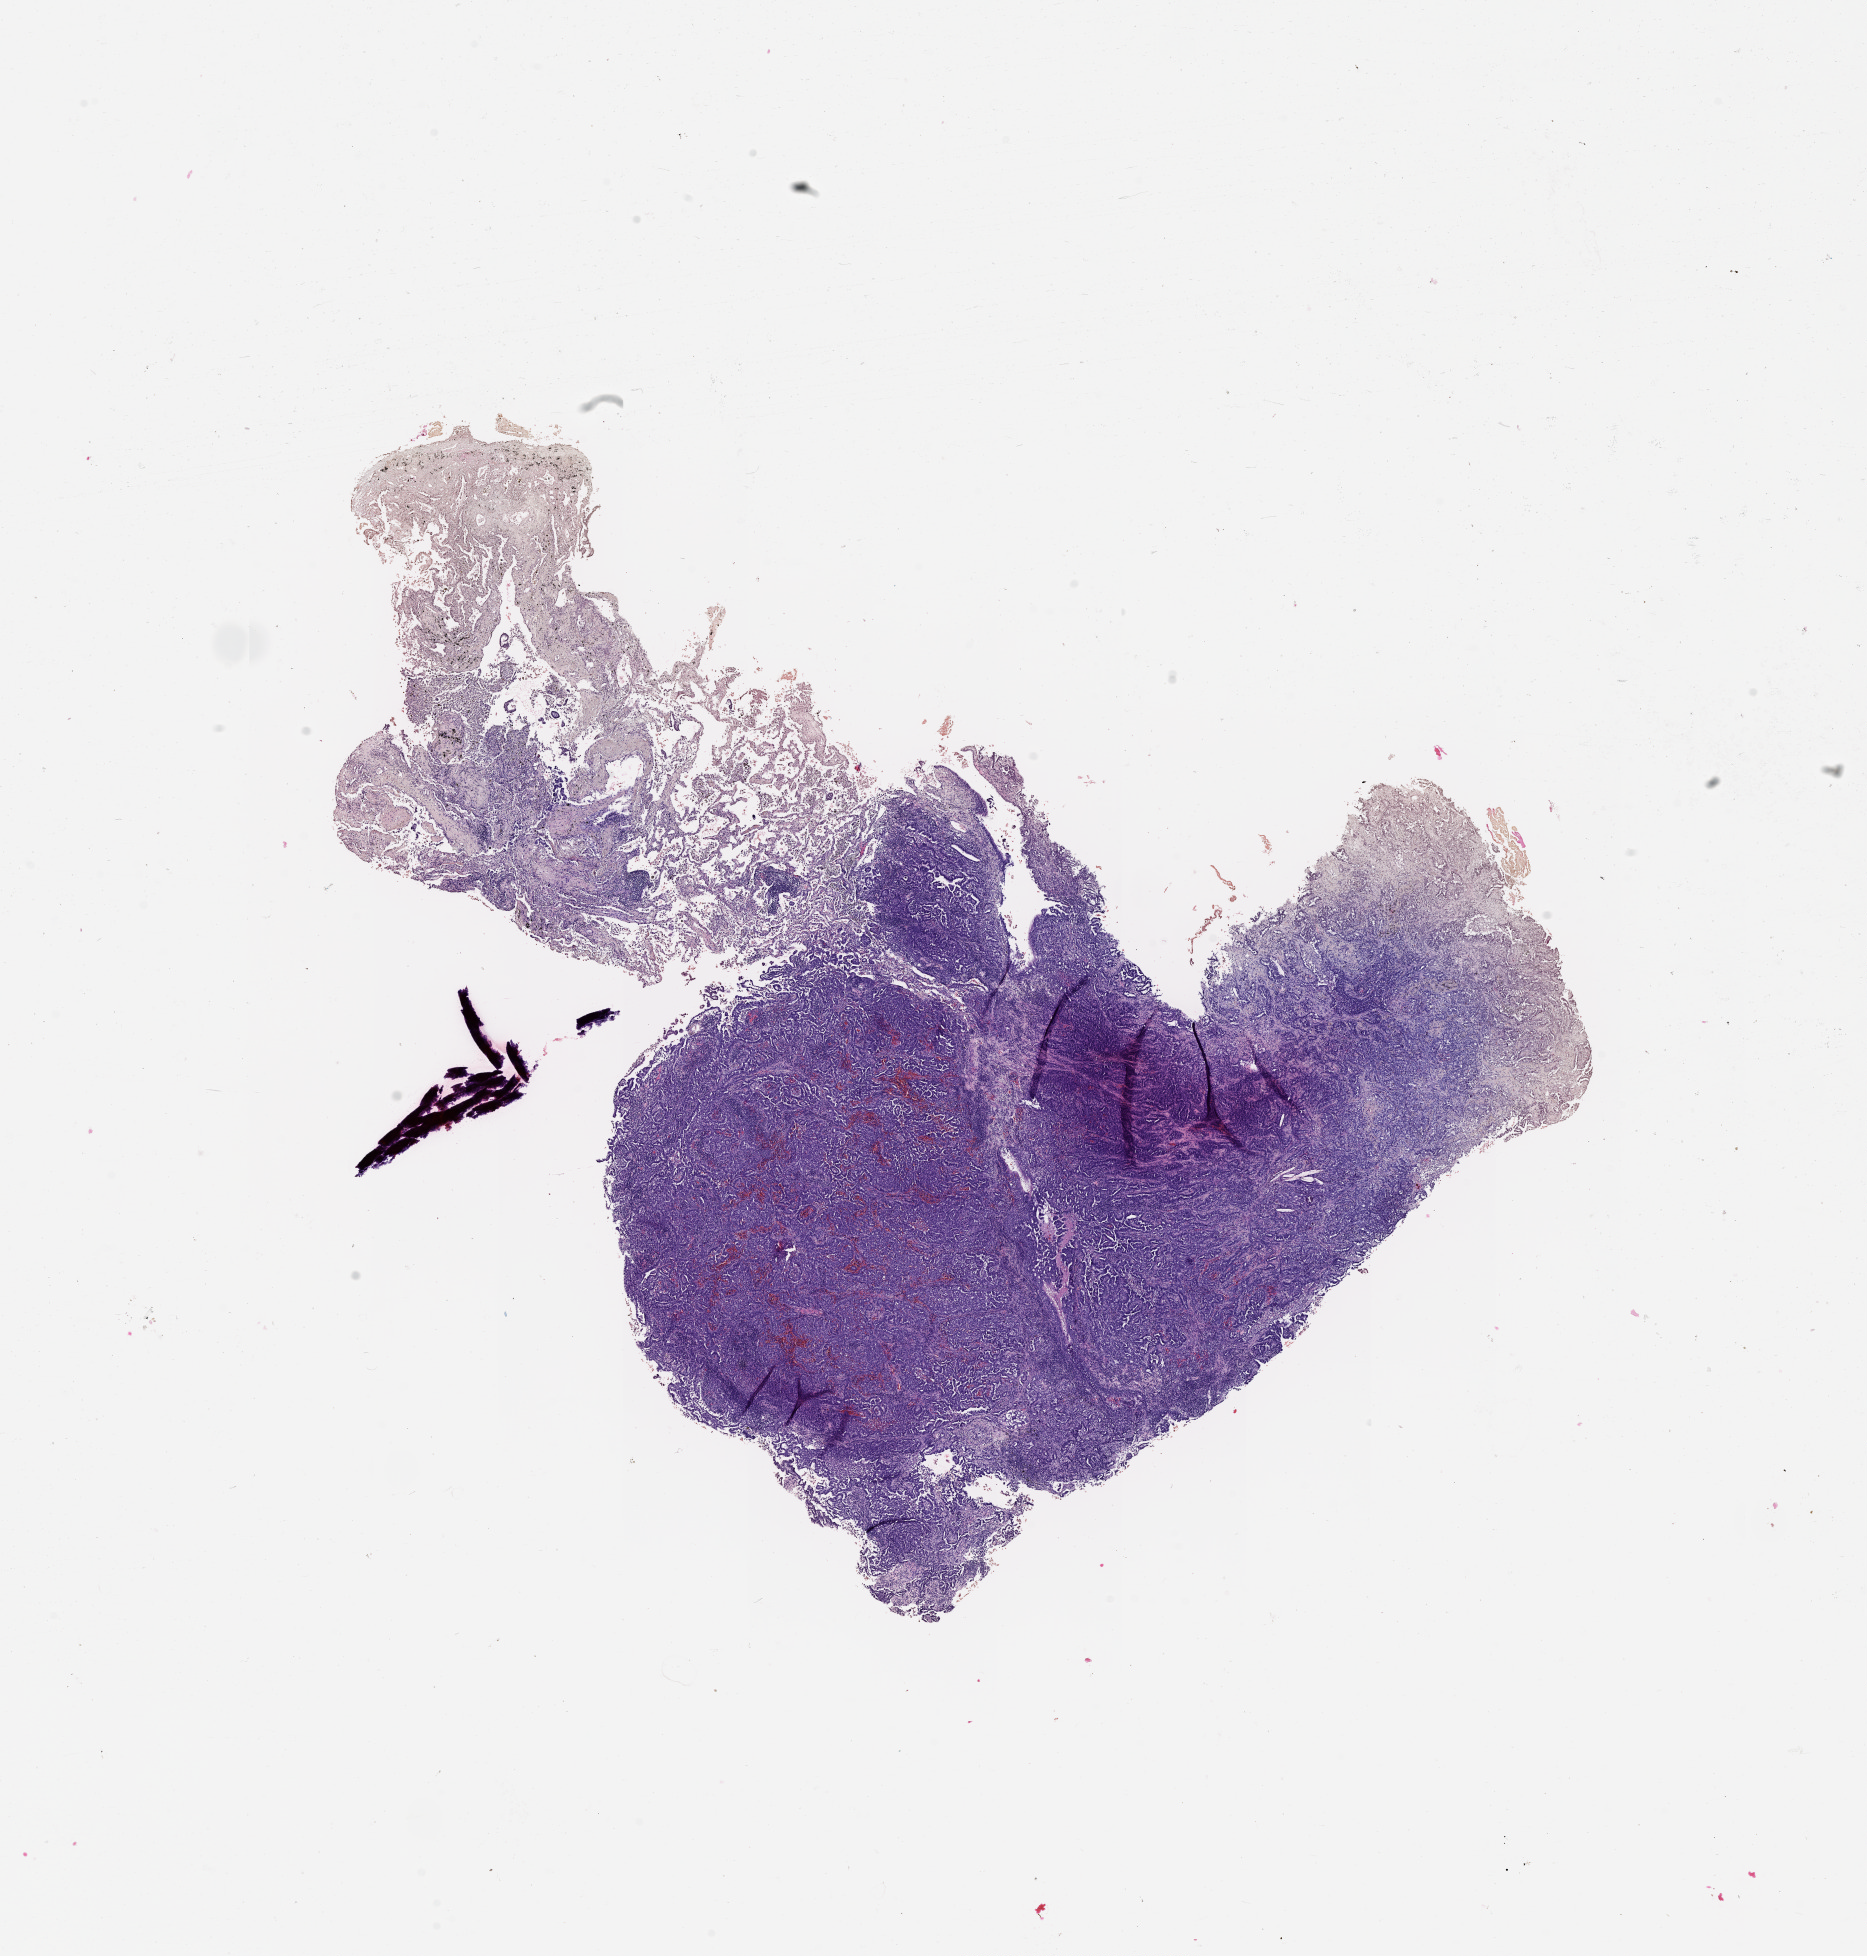
Whole-slide histology image, Hematoxylin and eosin (H&E) stained — whole scanned area (about 15.0 x 15.7 mm) shown as a low-resolution overview; tumour tissue sample, lung. 68-year-old male patient. Histologic grade: G1 (well differentiated).
• diagnosis: Adenocarcinoma, NOS
• AJCC pathologic stage: IB